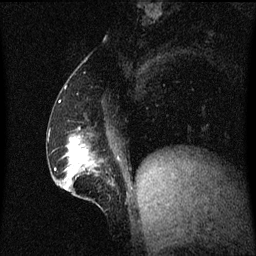
Breast MRI (dynamic contrast-enhanced), one sagittal slice. Slice 23 of 60 in the series (ordered by position). Dynamic contrast-enhanced series, image 2 of 3 at this slice position (ordered by acquisition). 1.5 T. TE 4.2 ms, TR 8.4 ms. 256 × 256 image matrix, field of view 200 × 200 mm. Patient: female, 52 years. From the clinical record (not read from this slice): setting: breast cancer imaged before/during neoadjuvant chemotherapy; receptor status: HER2-positive.
Structures marked on this image (semi-automatic segmentation, software-assisted and operator-edited):
- analysis volume of interest (the breast-tissue region the enhancement analysis was run in; not a lesion): bounding box (x1, y1, x2, y2) in pixels: (62, 132, 122, 201)
- tumour enhancement mask (voxels above the 70 % enhancement threshold inside the analysis volume of interest): (66, 140, 89, 191)